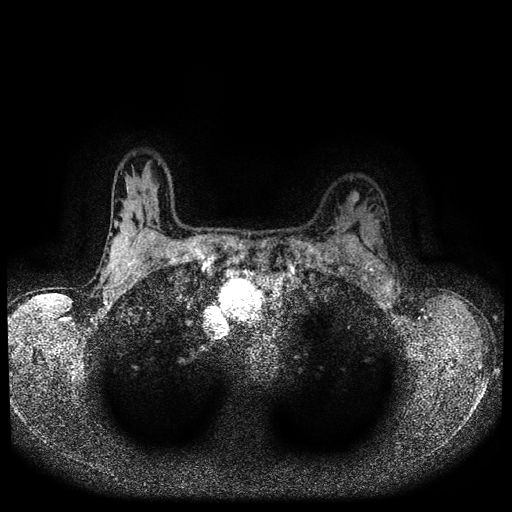
Breast MRI (dynamic contrast-enhanced, multi-phase), one axial slice; position 78 of 116 along the scan axis; dynamic contrast-enhanced series, time point 2 of 5 at this slice position (early post-contrast); 1.5 T; TE 2.7 ms, TR 5.4 ms; 2 mm slice thickness; 512 × 512 image matrix, field of view 330 × 330 mm. Patient: female, 32 years.
Outlined on this slice (semi-automatic segmentation, software-assisted and operator-edited):
- breast lesion (labelled benign in the annotation): box from (x=347, y=190) to (x=359, y=207) px